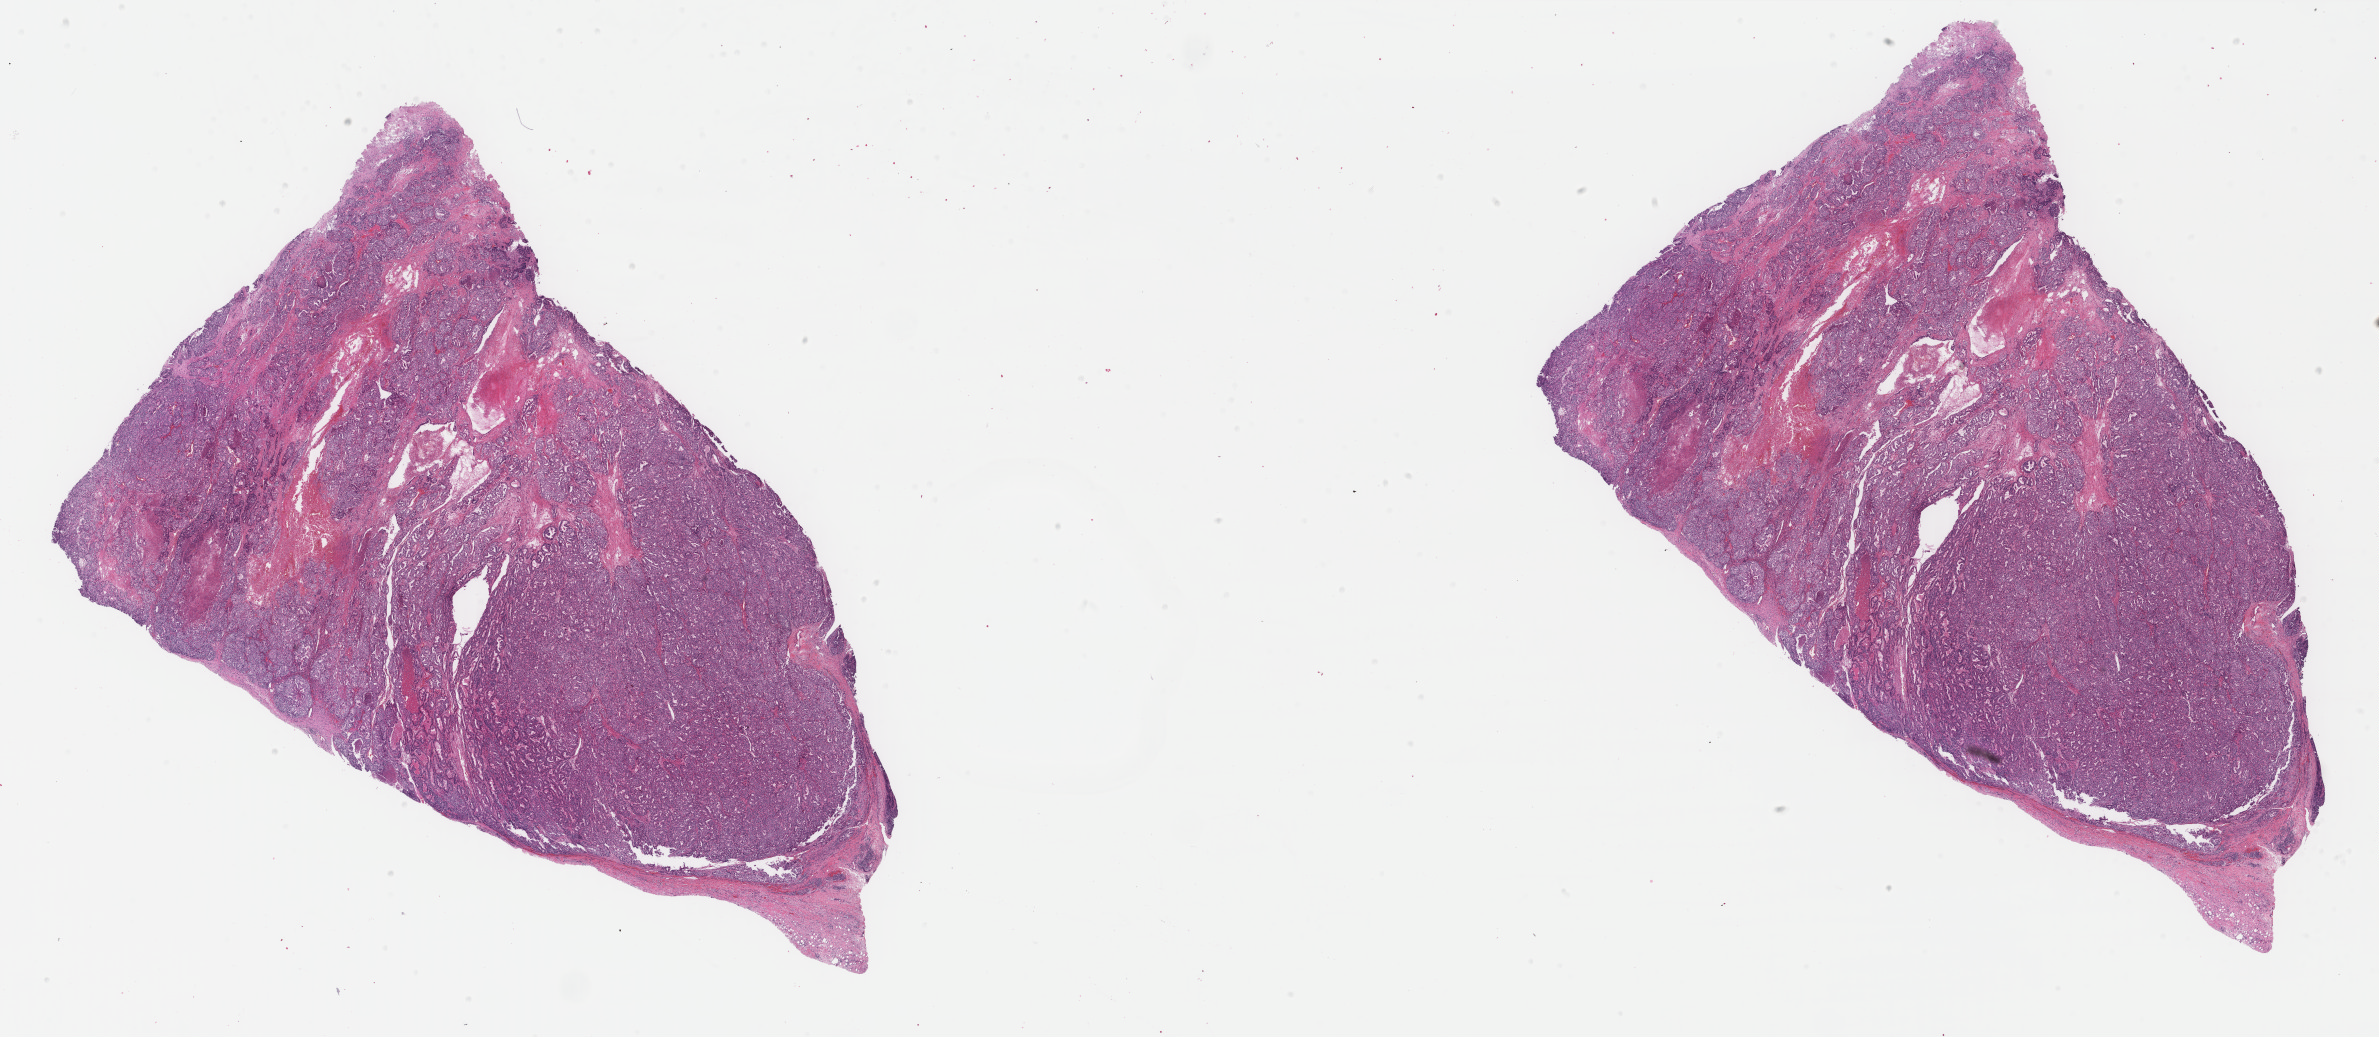
Digitized H&E-stained tissue section (whole slide) — a low-resolution overview of the entire scanned area, about 37.8 x 16.5 mm (acquisition: 40x scan). Formalin-fixed paraffin-embedded (FFPE) diagnostic section. Primary tumour sample from the breast. Female patient; age at initial diagnosis 41 years.
• TNM: T4 N0 M0
• histologic diagnosis: Infiltrating duct carcinoma, NOS
• laterality: left
• AJCC pathologic stage: IIIB (7th edition)